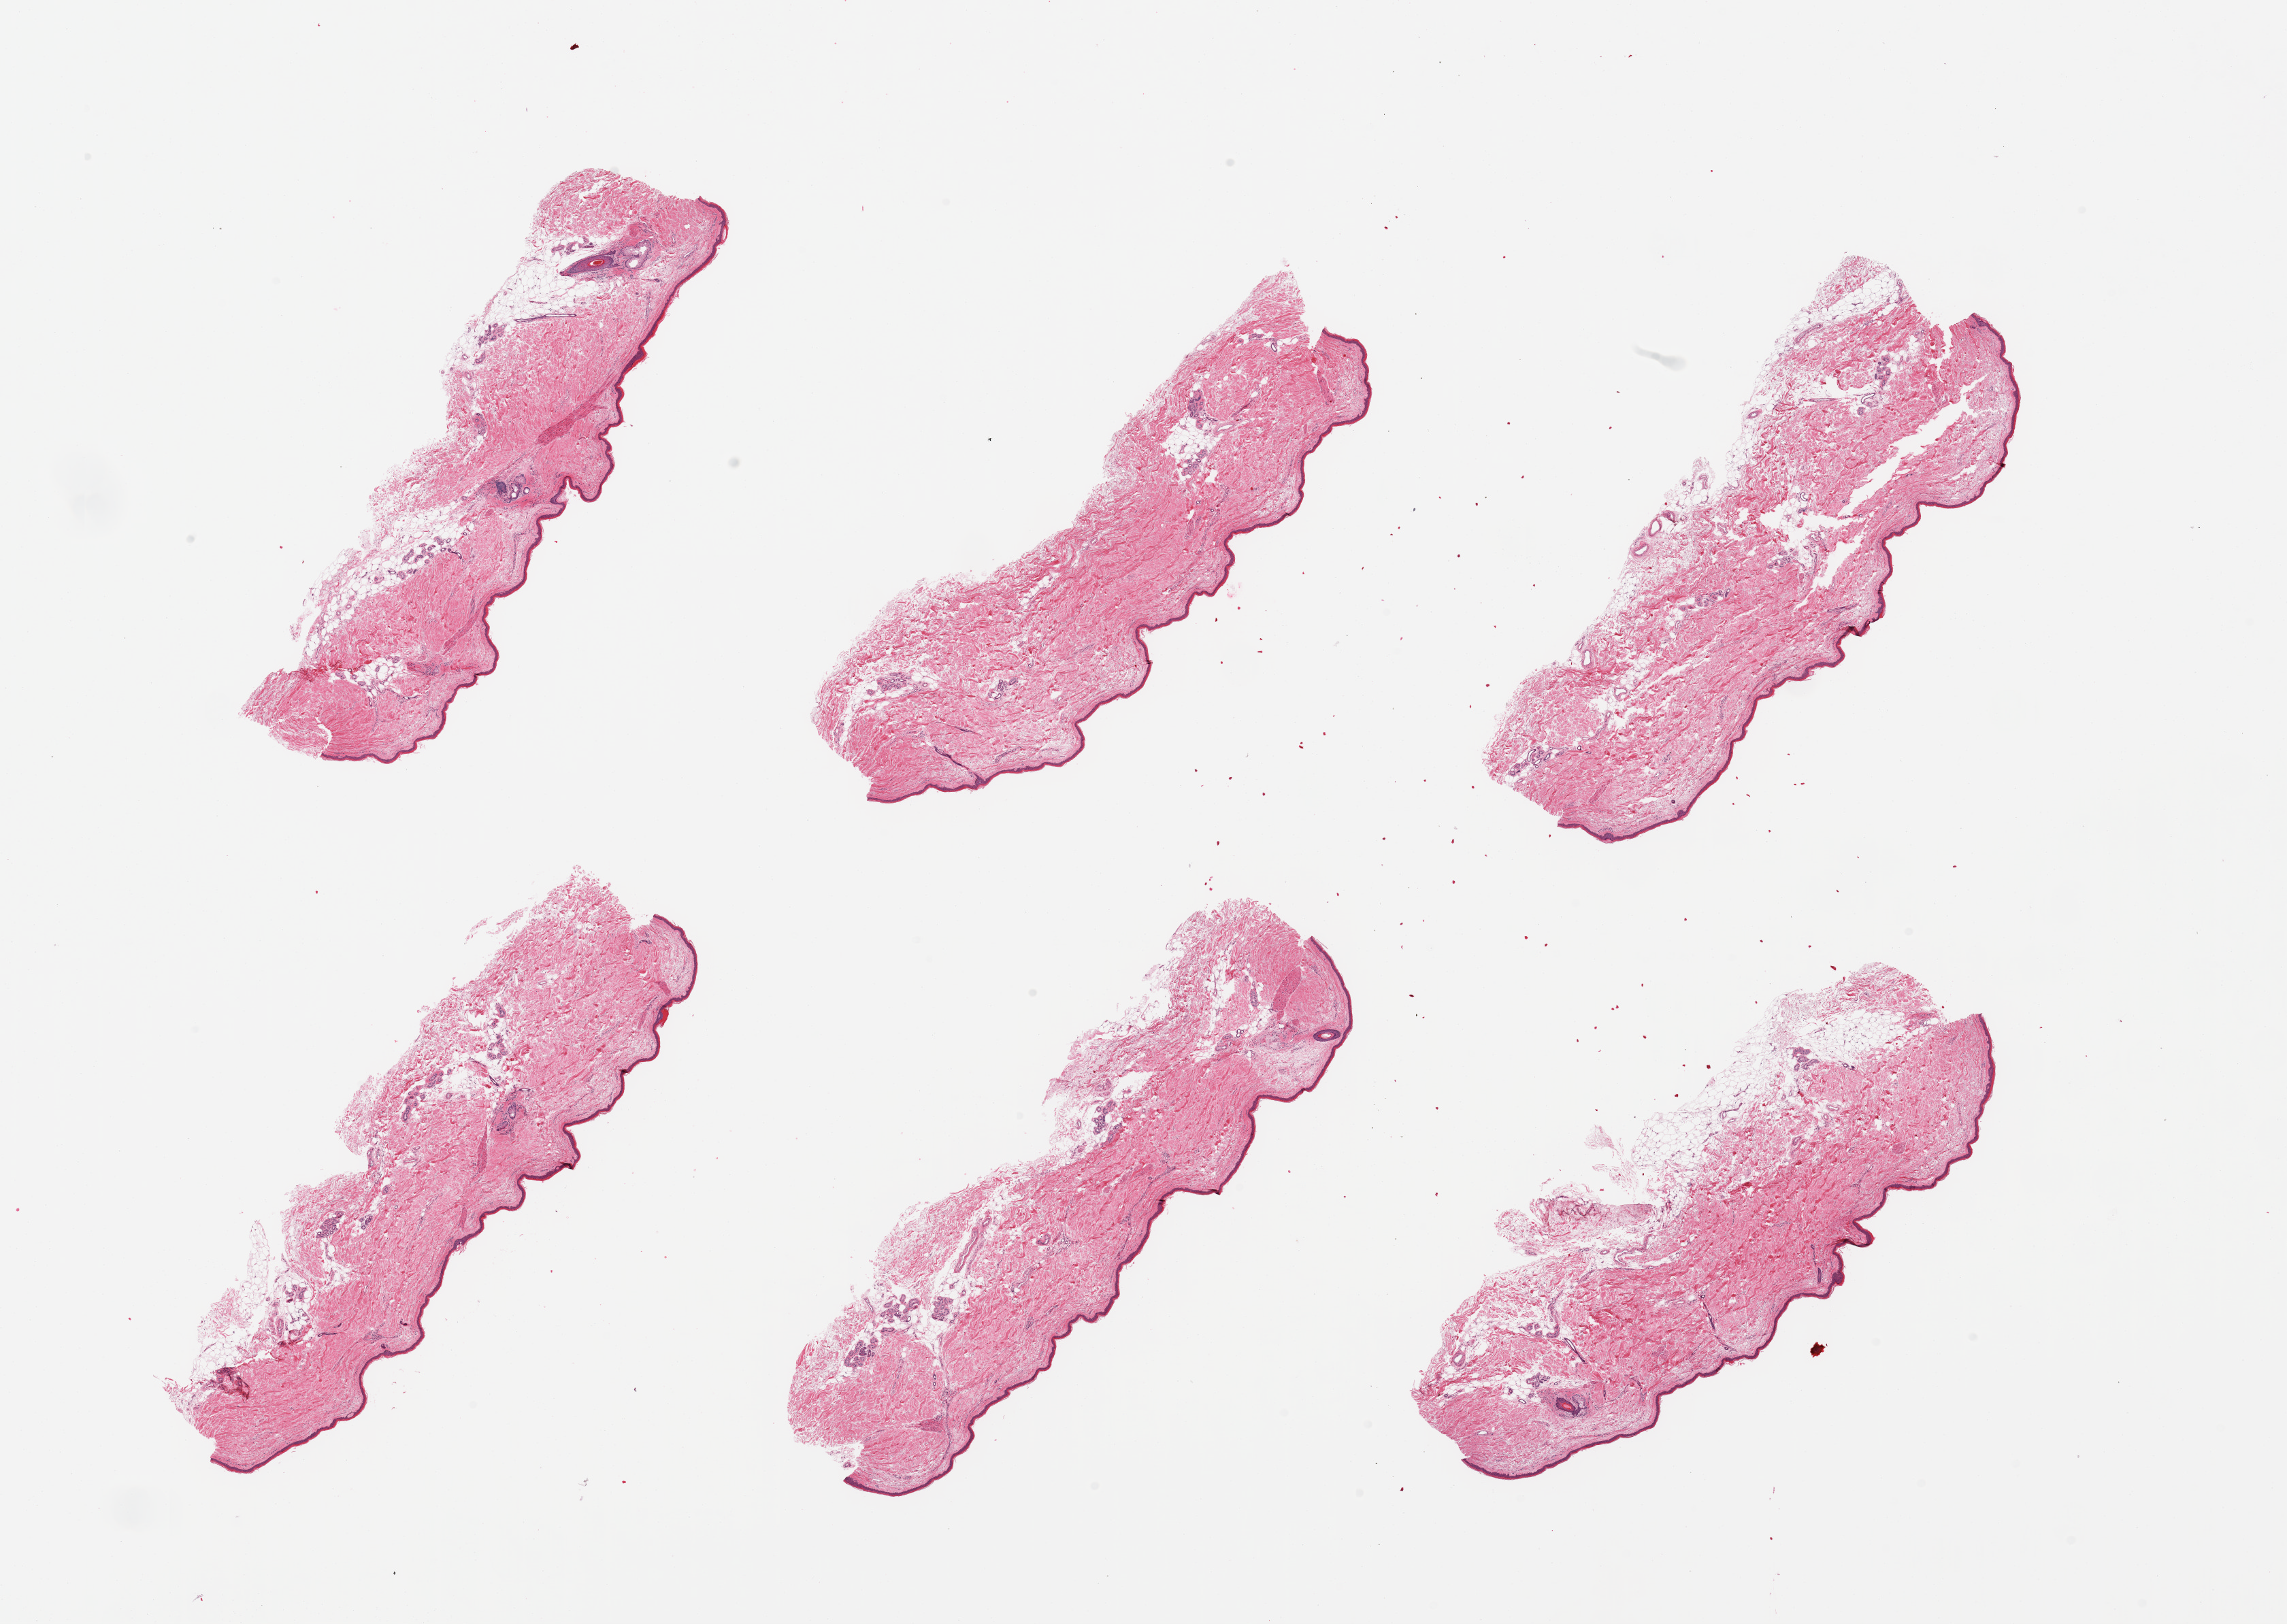
Hematoxylin and eosin (H&E) whole-slide image — whole scanned area (about 26.6 x 18.9 mm, from a 20x scan) shown as a low-resolution overview, PAXgene-fixed paraffin-embedded (PFPE) section, sampled site (target tissue): skin of lower leg, tissue donor sample. Male donor.
- reviewer comment on this tissue sample: 6 pieces; adherent dermal fat focally up to ~0.5mm; squamous epithelium is ~20-3- microns